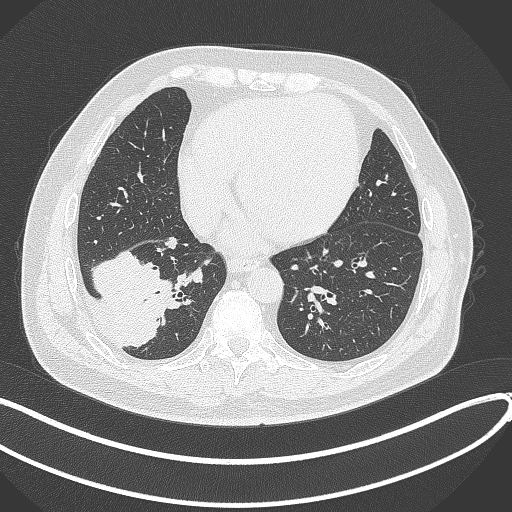
Chest CT, one axial slice. Slice 119 of 360 in the series (ordered by position). Reconstruction kernel B70f. Lung window (W 1500 / L -600 HU). 1 mm slice thickness. 512 × 512 image matrix, field of view 400 × 400 mm. Patient: male, 59 years.
Annotated regions visible in this slice (rectangle marked by the reading radiologist):
- lung tumour (recorded histology: adenocarcinoma): bounding box (x1, y1, x2, y2) in pixels: (85, 244, 186, 351)